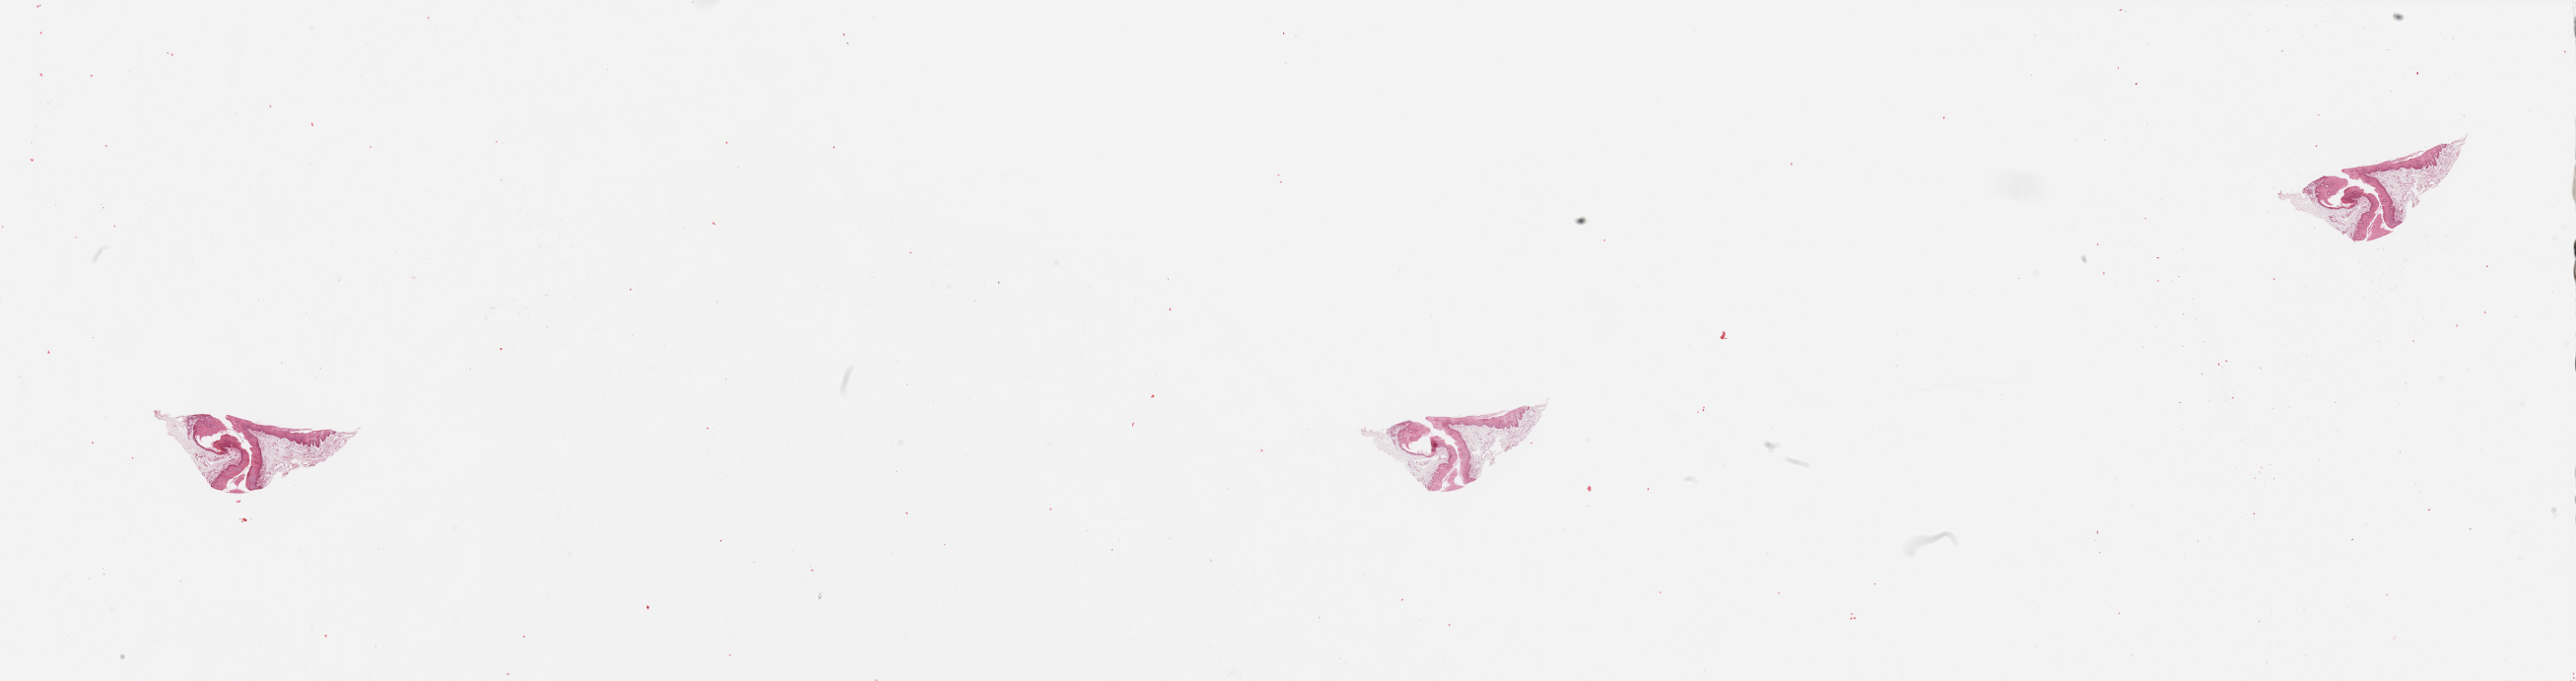
Digitized Hematoxylin and eosin (H&E) stained tissue section (whole slide), a low-resolution overview of the entire scanned area, about 41.3 x 10.9 mm (acquisition: 20x scan), head and neck, normal (non-tumour) tissue. 42-year-old male patient.
- this section: normal (non-tumour) tissue from the same patient
- patient diagnosis: Squamous cell carcinoma, NOS (larynx, NOS)